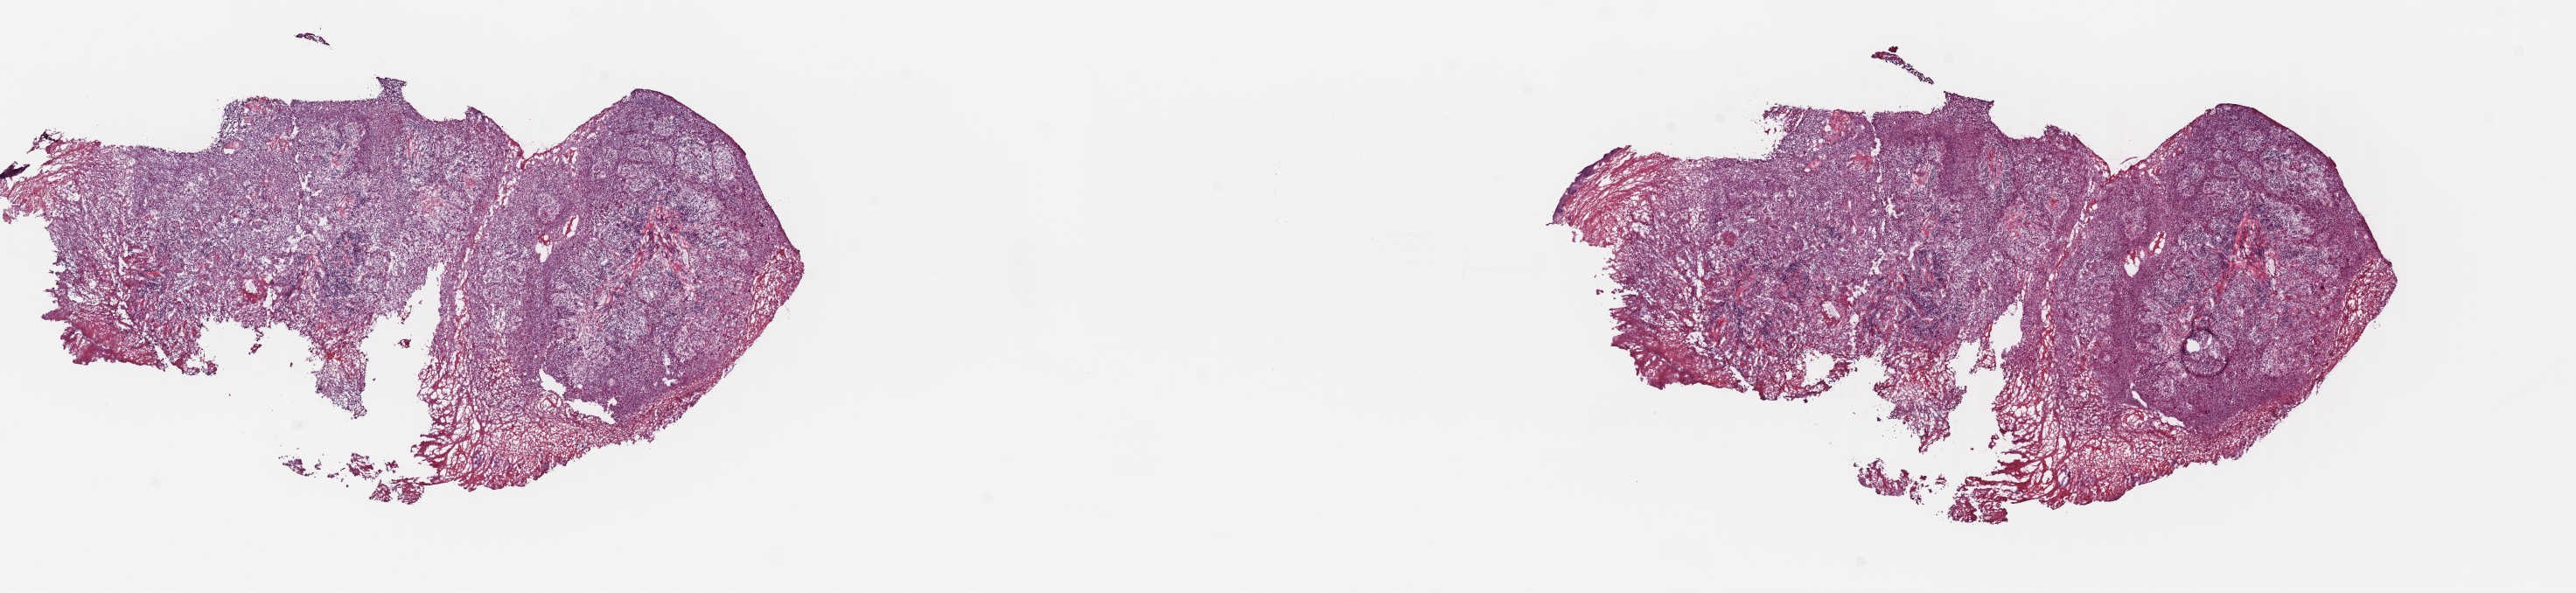
Digitized H&E tissue section (whole slide), low-resolution overview of the scanned area, about 23.1 x 5.3 mm (acquisition: 40x scan). Frozen section. Head and neck, primary tumour sample. Male patient; age at initial diagnosis 46 years. Histologic grade: G2 (moderately differentiated). Pathologist review of this section (percent, as recorded): tumour cells 80%, tumour nuclei 70%, normal cells 0%, stromal cells 20%, necrosis 0%. Infiltration values recorded for this section: lymphocyte infiltration 0%, monocyte infiltration 0%, neutrophil infiltration 0%.
• laterality: left
• AJCC pathologic stage: II (7th edition)
• diagnosis: Squamous cell carcinoma, NOS (tonsil, NOS)
• TNM: T2 N0 MX